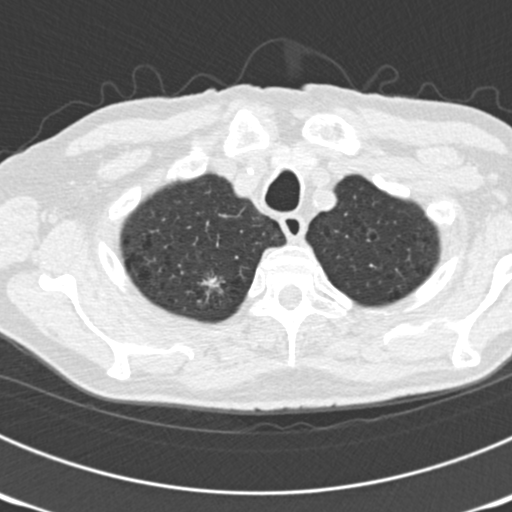
Low-dose screening chest CT, one axial slice. Slice 158 of 177 in the series (ordered by position). Reconstruction kernel B30f. 120 kVp. Lung window (W 1500 / L -600 HU). 2 mm slice thickness. 512 × 512 image matrix, field of view 300 × 300 mm.
Outlined on this slice (manually delineated by an expert):
- lesion 3 (nodule, upper lobe of right lung): box from (x=199, y=276) to (x=226, y=294) px